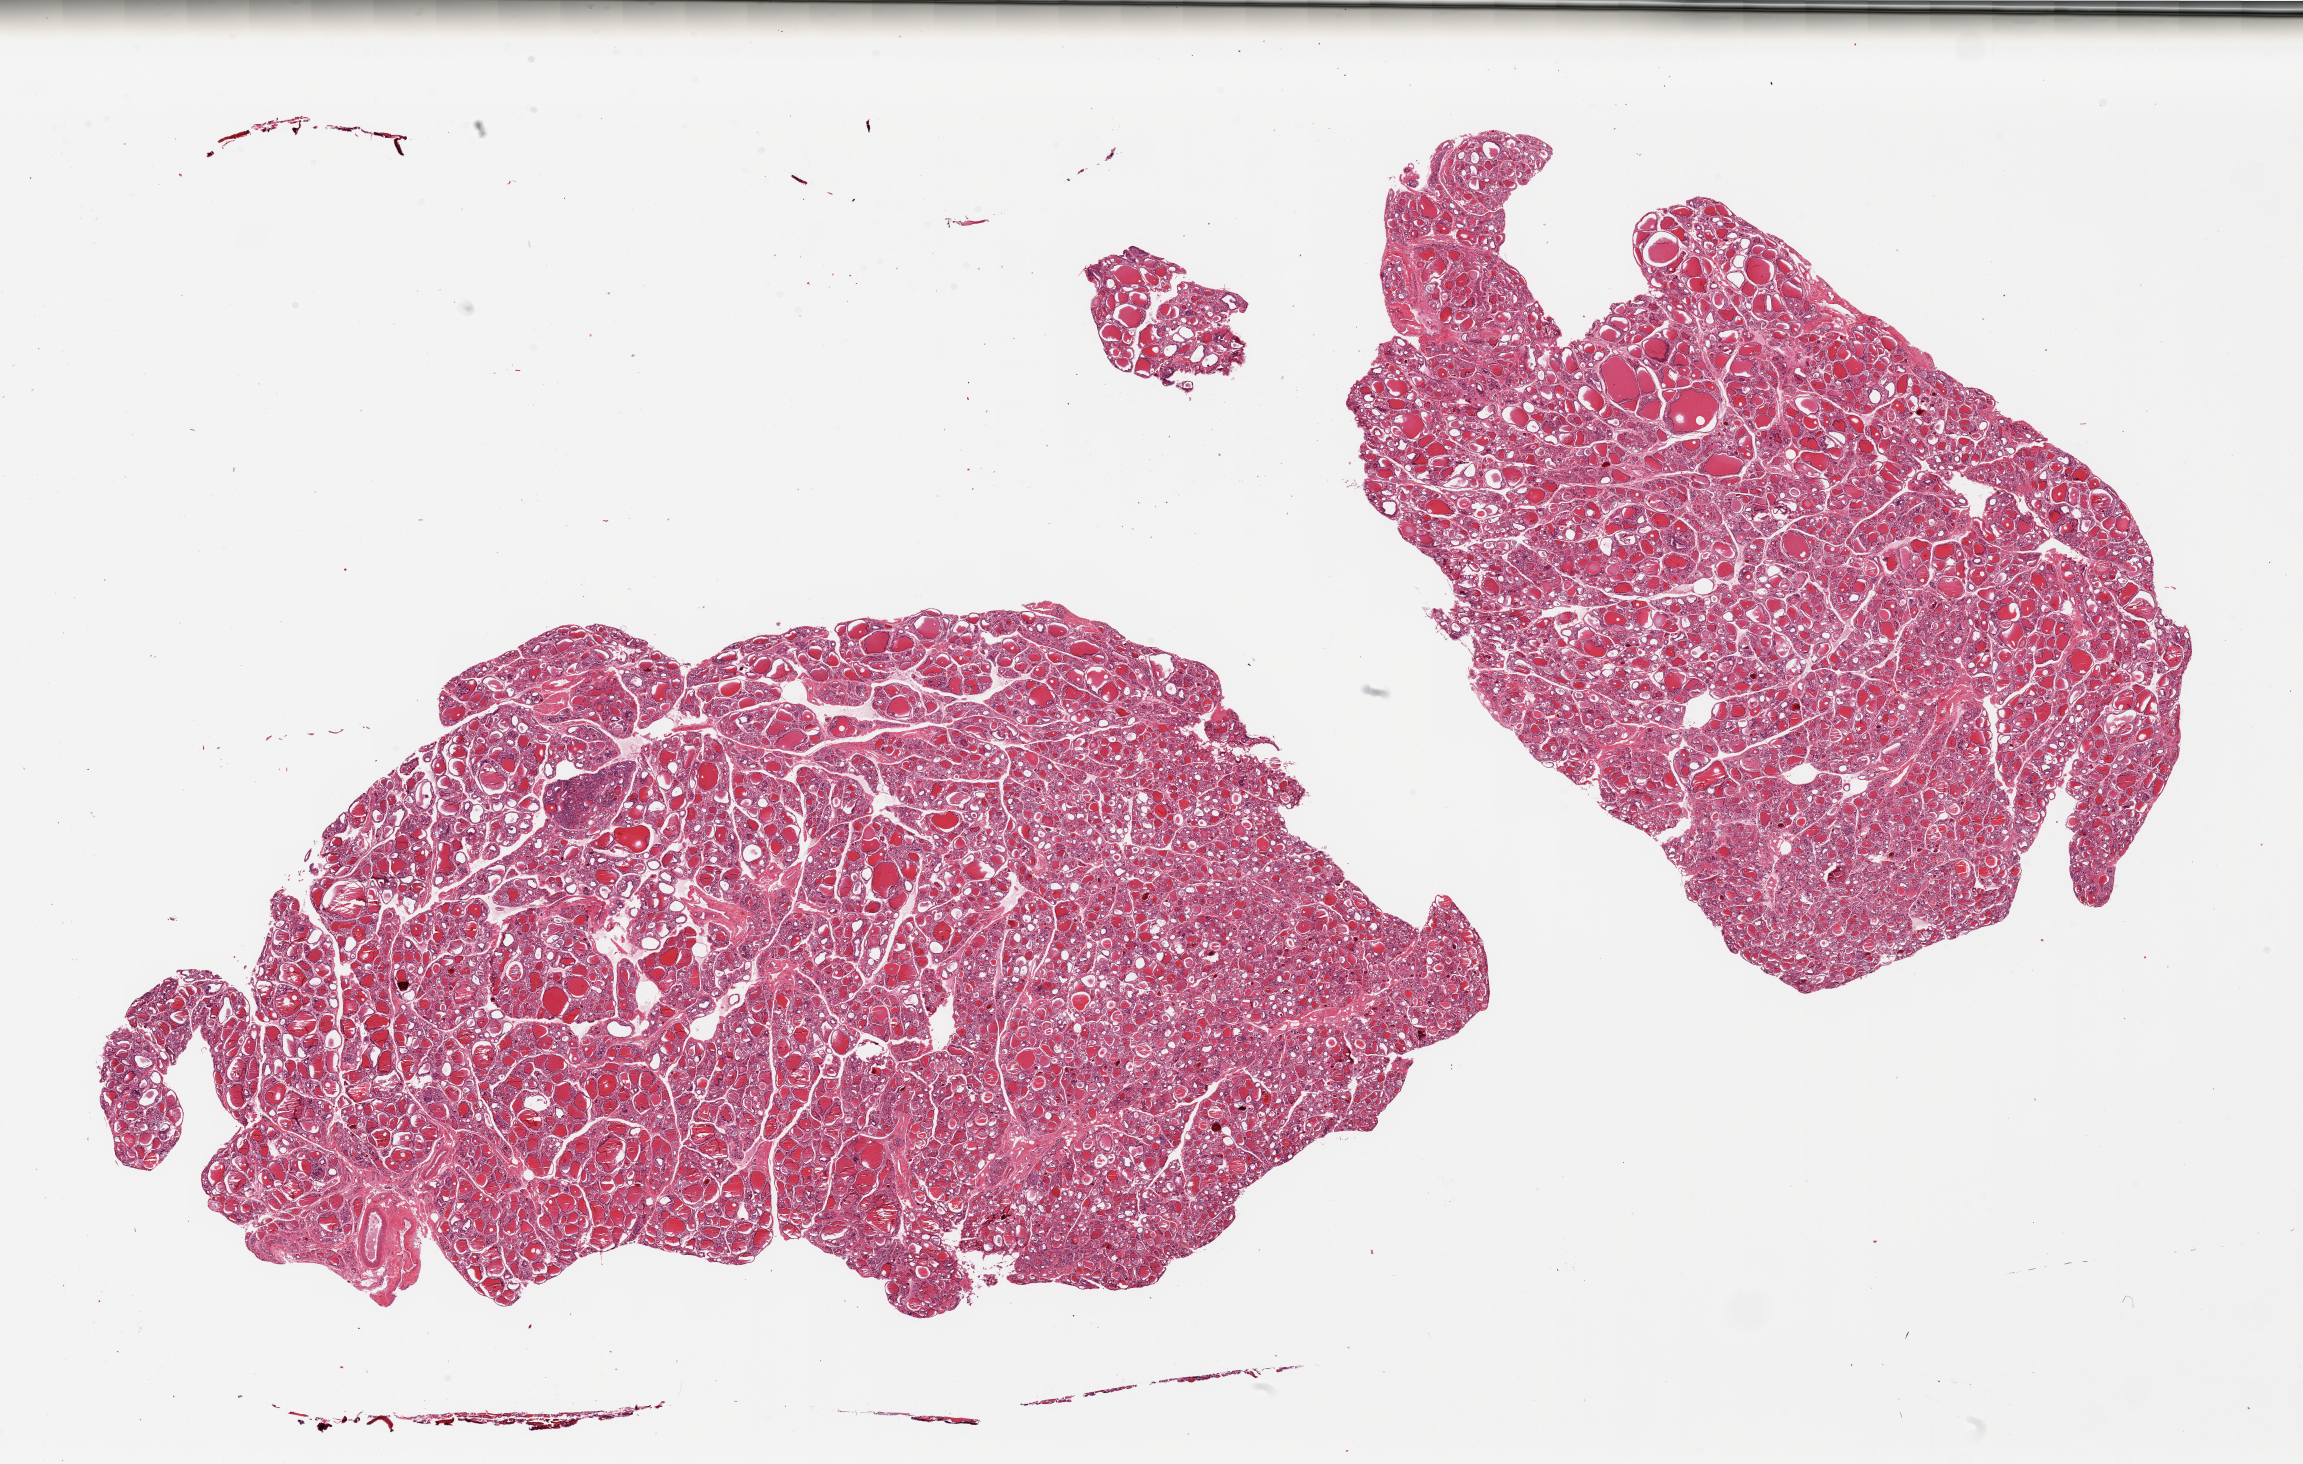
Whole-slide image, hematoxylin and eosin (H&E) stain, low-resolution overview of the scanned area, about 36.4 x 23.2 mm, PAXgene-fixed, paraffin-embedded tissue, target tissue: thyroid, donor tissue sample. Male donor.
Review note (as recorded): 2 pieces.